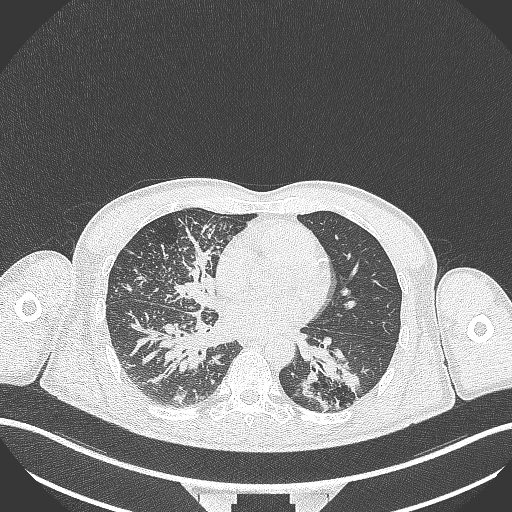
Chest CT, one axial slice. Slice 140 of 348 in the series (ordered by position). Reconstruction kernel B70f. Lung window (W 1500 / L -600 HU). 1 mm slice thickness. 512 × 512 image matrix, field of view 400 × 400 mm. Patient: male, 49 years. From the clinical record (not read from this slice): clinical TNM (as recorded): T2b N1 M0.
Structures marked on this image (bounding box drawn by a radiologist):
- lung tumour (recorded histology: adenocarcinoma): bounding box [x1, y1, x2, y2] px = [292, 337, 365, 410]